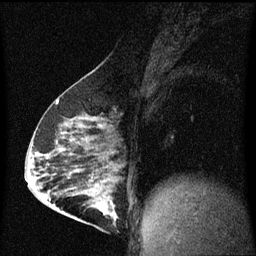
Breast MRI (dynamic contrast-enhanced), one sagittal slice; position 32 of 60 along the scan axis; dynamic contrast-enhanced series, image 2 of 3 at this slice position (ordered by acquisition); 1.5 T; TE 4.2 ms, TR 8 ms; 256 × 256 image matrix. Female patient, age 63 years.
Structures marked on this image (semi-automatically segmented with operator editing):
- analysis volume of interest (the breast-tissue region the enhancement analysis was run in; not a lesion): bounding box [x1, y1, x2, y2] px = [88, 182, 121, 229]
- tumour enhancement mask (voxels above the 70 % enhancement threshold inside the analysis volume of interest): [100, 196, 117, 219]